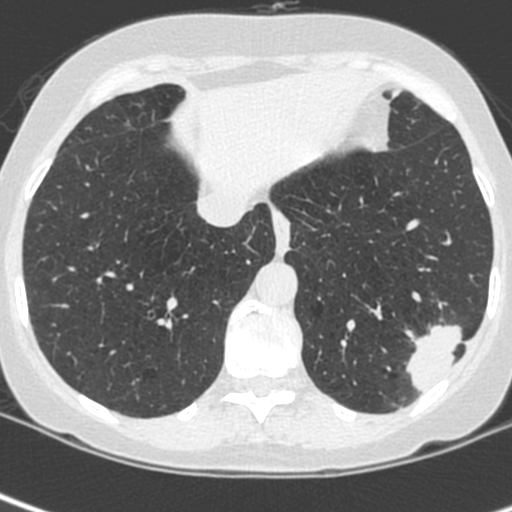
Axial slice from a low-dose chest CT screening exam, baseline screening round, lung window (W 1500 / L -600 HU), 1.3 mm slice thickness, standard (soft-tissue) reconstruction kernel (C), 120 kVp, slice 176 of 252 in the series, 512 × 512 image matrix. Female participant, aged 56 years at enrolment.
- Expert-annotated lung lesion, bounding box <403,311,478,387> (left, top, right, bottom; pixels).
- The exam's reader record, not a measurement of the box and not confirmed to be the same lesion: non-calcified nodule or mass ≥4 mm, left lower lobe, 37 × 29 mm, spiculated (stellate) margins, ground glass attenuation.
- Lung cancer was diagnosed 91 days after this screen: squamous cell carcinoma, NOS, left lower lobe, poorly differentiated (G3), stage IIIA (AJCC 6th edition), 35 mm at pathology.